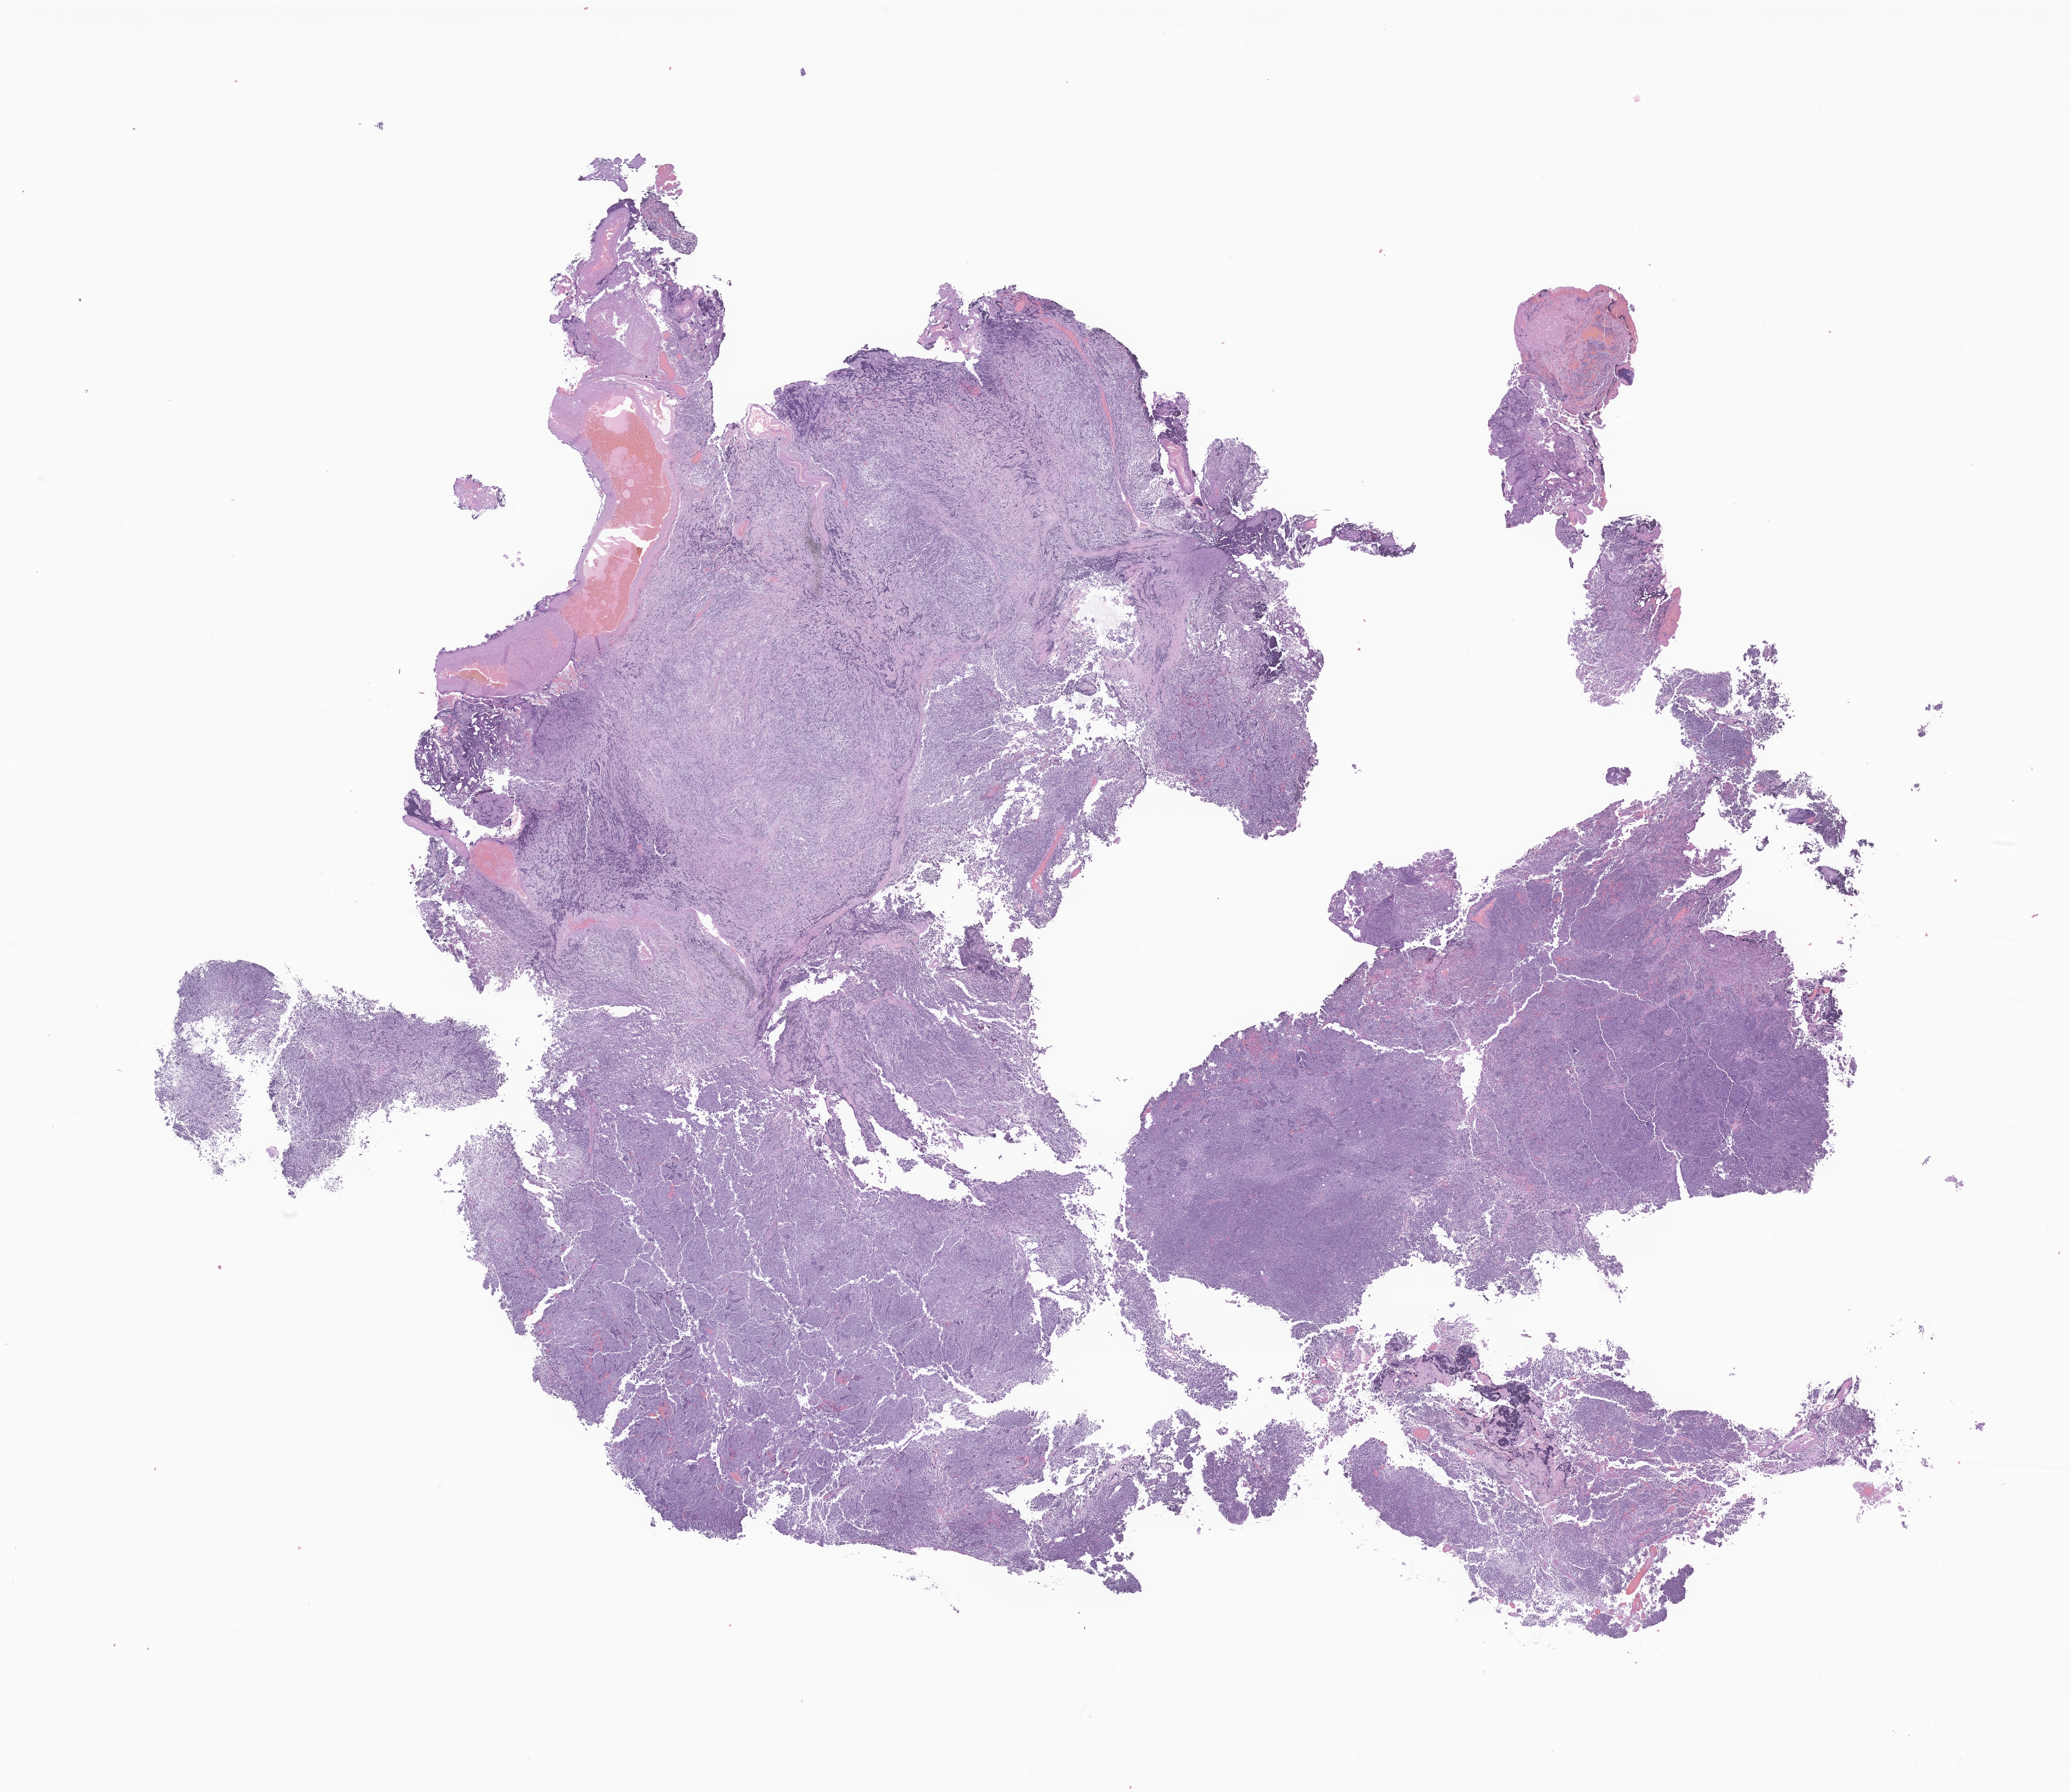
Digitized H&E-stained section of tumor tissue from the brain, a low-resolution overview of the entire scanned area, about 25.1 x 21.7 mm, formalin-fixed, paraffin-embedded (FFPE) tissue. Male patient, age 135 months (11 years 3 months).
Diagnosis: Medulloblastoma, NOS.